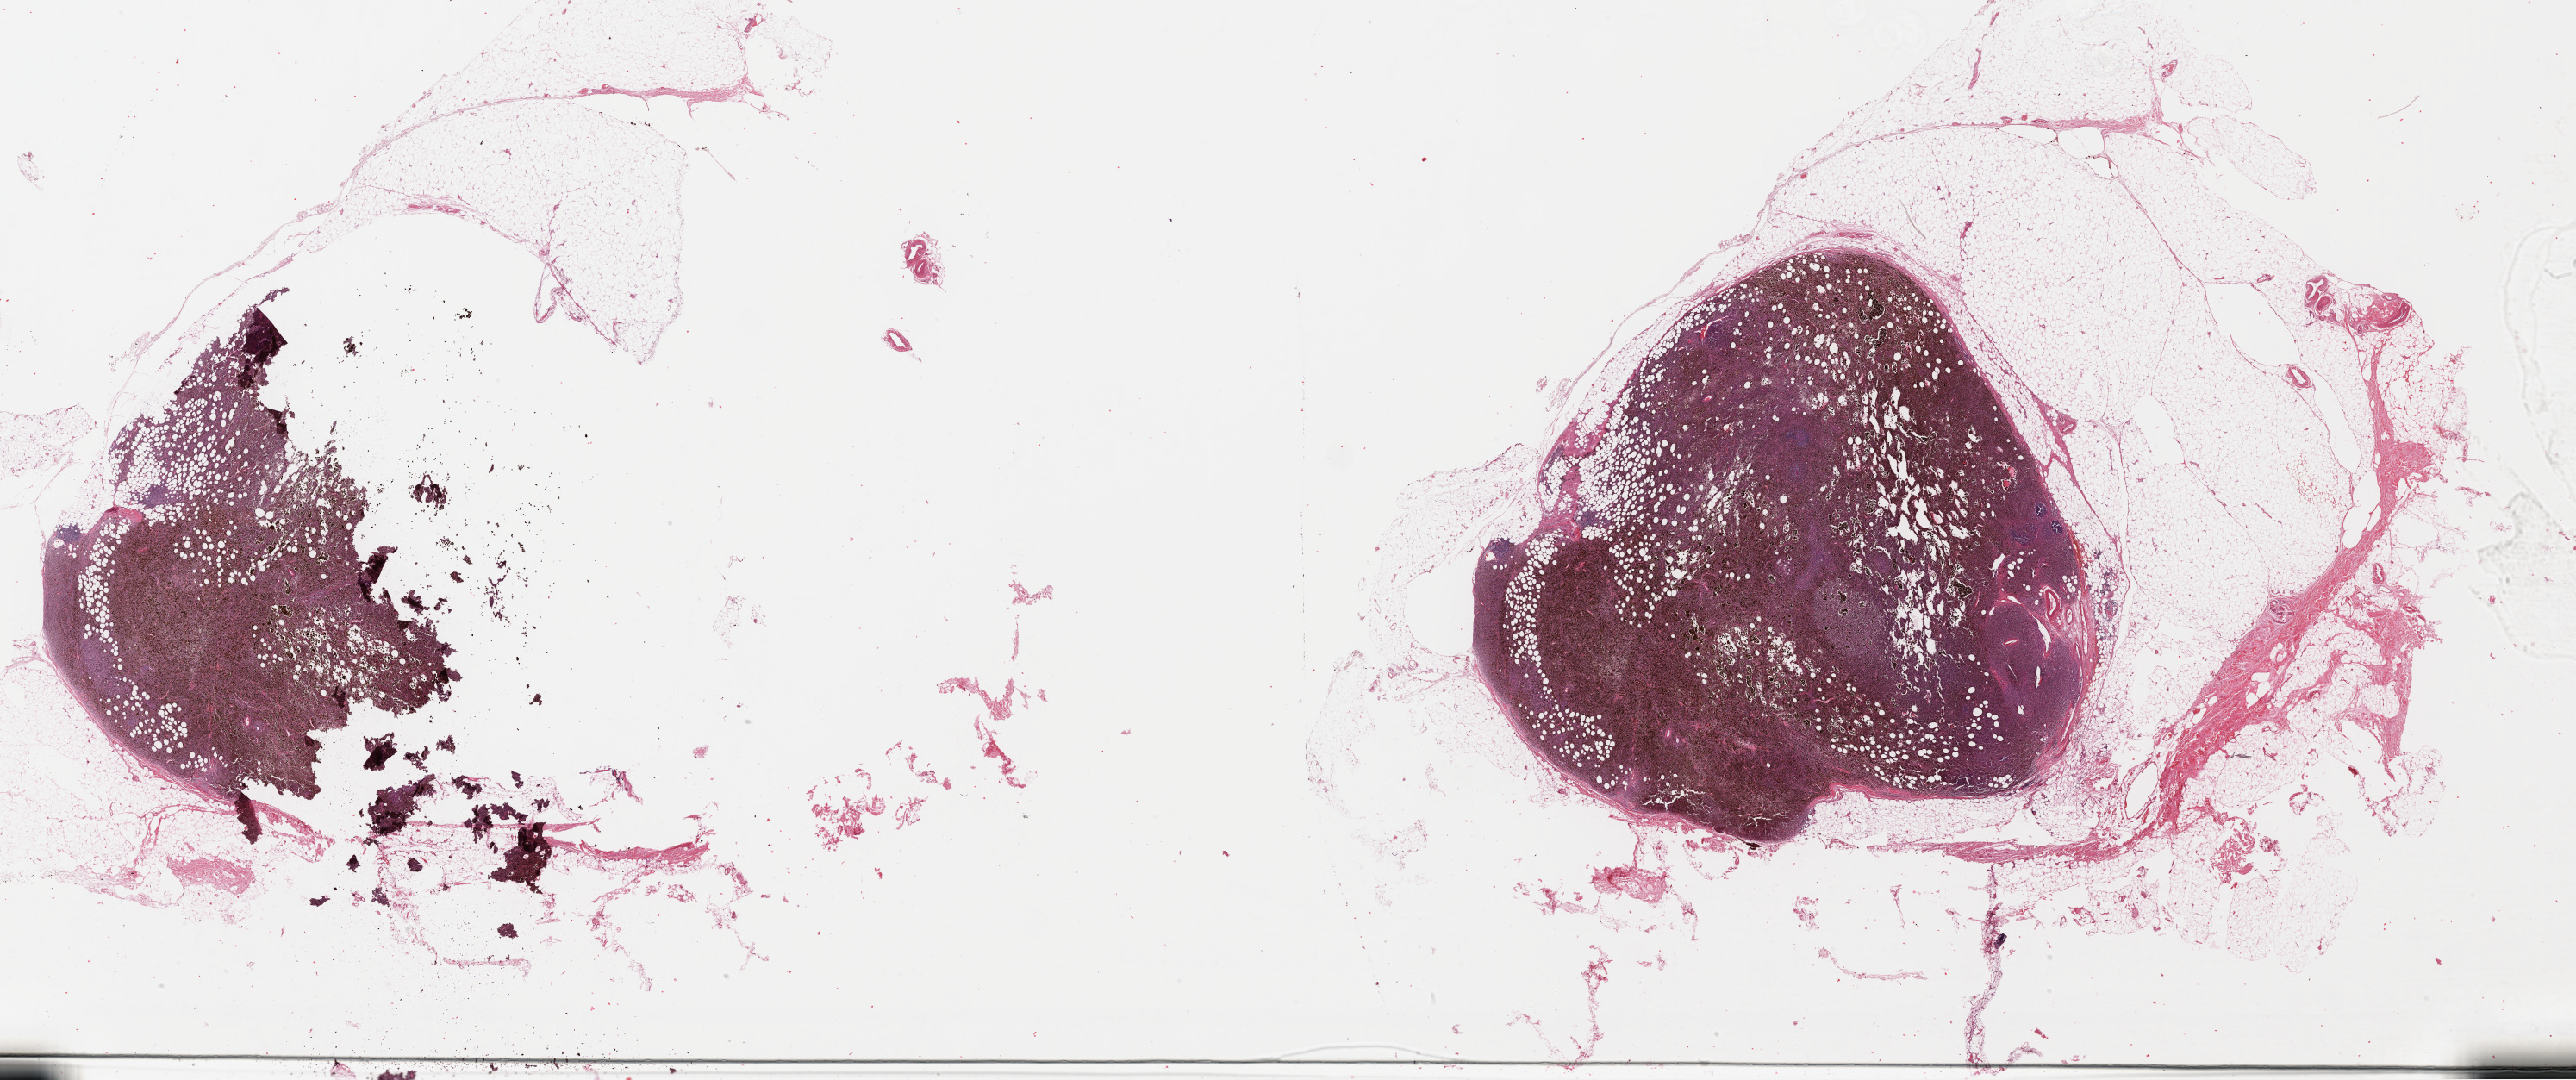
Hematoxylin and eosin (H&E) stained whole-slide image, a low-resolution overview of the entire scanned area, about 47.0 x 19.7 mm (from a 40x scan). Formalin-fixed paraffin-embedded (FFPE) diagnostic section. Metastatic tumour sample, sampled site: lymph node. Patient: male, age at initial diagnosis 52 years.
This section: metastatic tumour tissue. Patient diagnosis: Malignant melanoma, NOS.